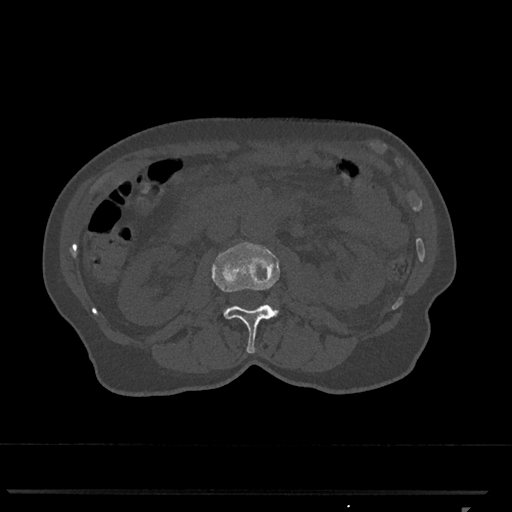
CT including the spine, one axial slice; slice 323 of 793 in the series (ordered by position); reconstruction kernel Br40s/3; 120 kVp; bone window (W 1800 / L 400 HU); 0.5 mm slice thickness; 512 × 512 image matrix, field of view 380 × 380 mm. Patient: female, 62 years. Case-level facts recorded for this patient, not image findings: primary cancer: renal.
Annotated regions visible in this slice (semi-automatically segmented with operator editing):
- L2 vertebra: bounding box <212,242,280,354> (left, top, right, bottom; pixels)